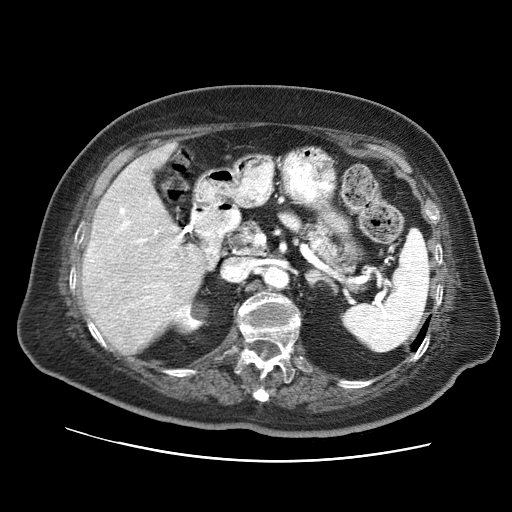
Contrast-enhanced abdominal CT (liver protocol), one axial slice; slice 35 of 73 in the series (ordered by position); soft-tissue window (W 400 / L 40 HU); 2.5 mm slice thickness; 512 × 512 image matrix, field of view 380 × 380 mm. From the clinical record (not read from this slice): diagnosis: hepatocellular carcinoma (patient treated with transarterial chemoembolisation; whether this scan precedes or follows treatment is not stated here); TNM stage (as recorded): Stage-I; Child-Pugh class: A; tumour differentiation: well differentiated.
Annotated regions visible in this slice (semi-automatic segmentation, software-assisted and operator-edited):
- liver parenchyma outside the tumour (the mass and vessels are separate outlines, so this box may not span the whole liver): bounding box [x1, y1, x2, y2] px = [82, 142, 218, 351]
- liver vessels: [87, 201, 216, 316]